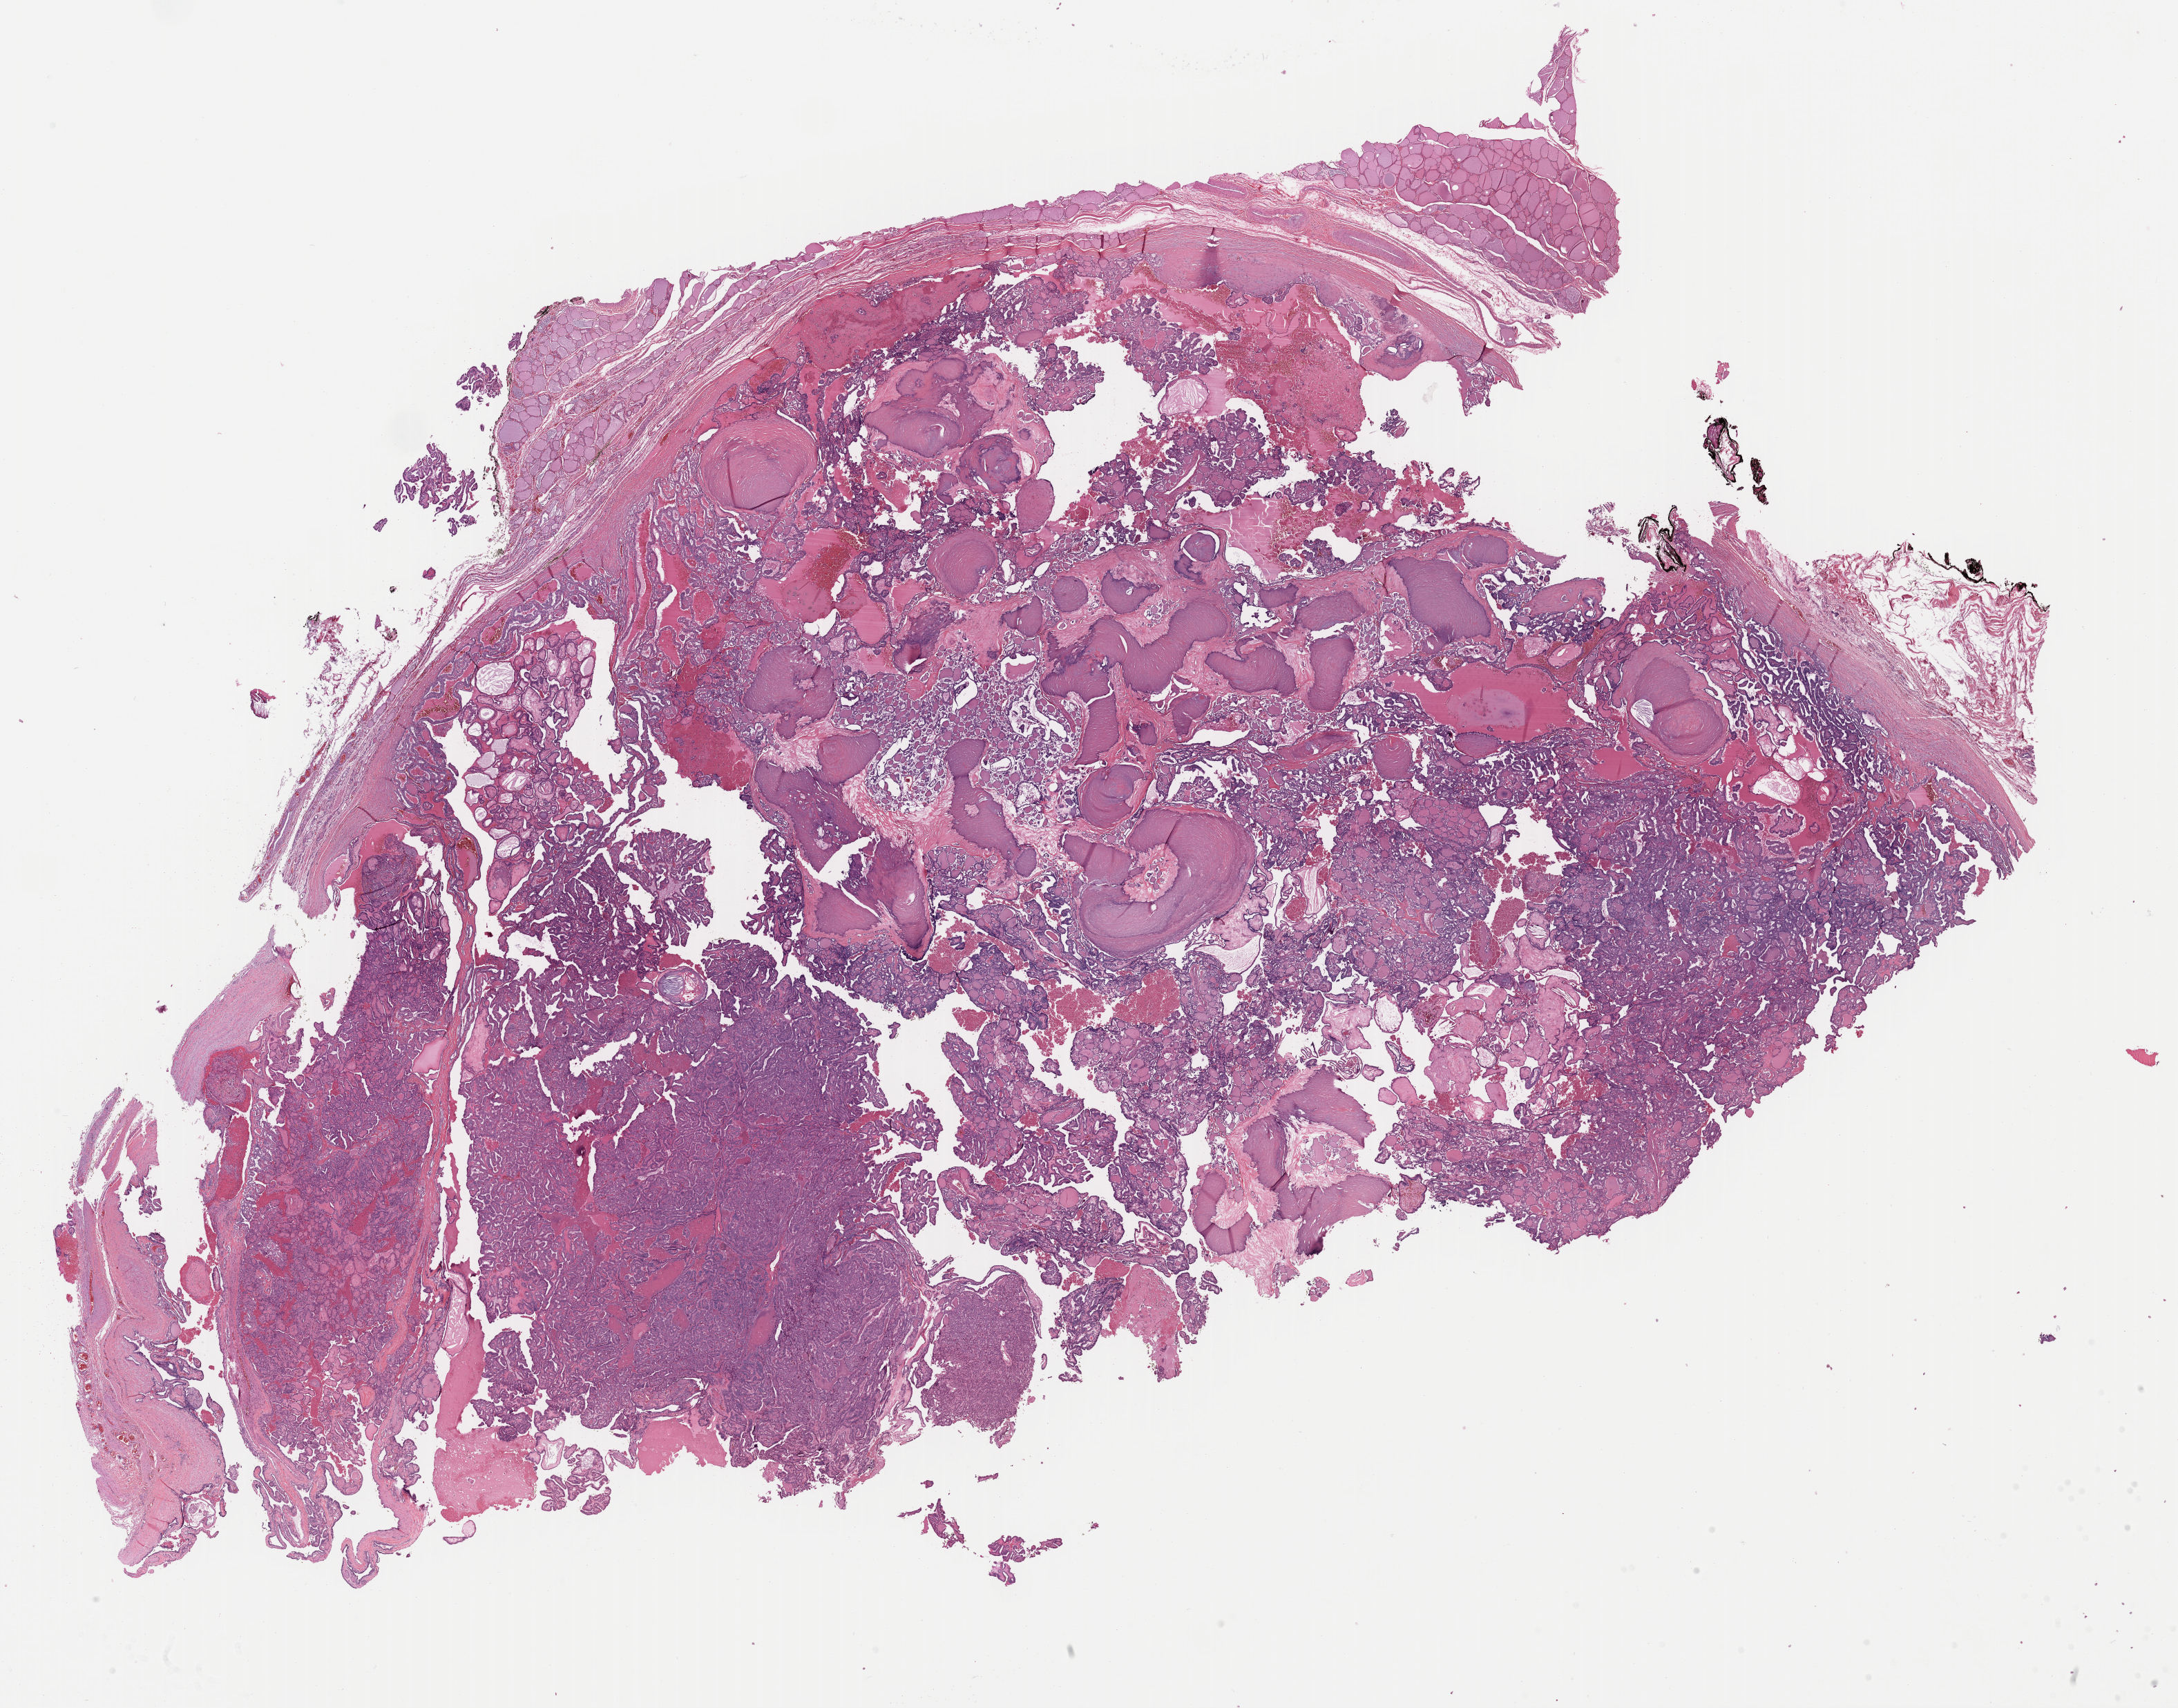
H&E whole-slide image, low-resolution overview of the scanned area, about 24.9 x 19.5 mm (from a 40x scan), FFPE section, primary tumour sample from the thyroid. Patient: male, age at initial diagnosis 47 years.
- laterality: midline
- diagnosis: Papillary adenocarcinoma, NOS (thyroid gland)
- lymph nodes positive (case pathology): 1 of 1 examined
- AJCC pathologic stage: III (7th edition)